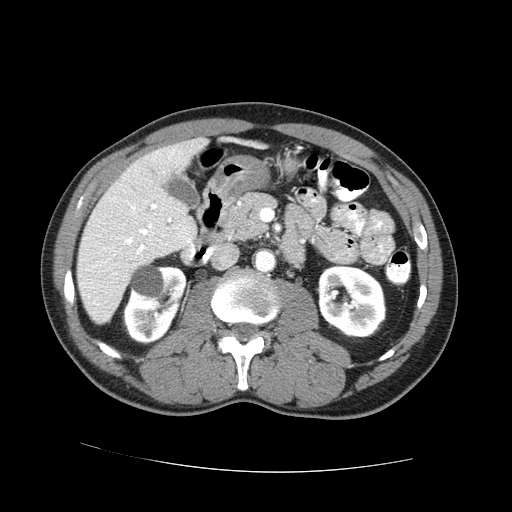
Contrast-enhanced abdominal CT (liver protocol), one axial slice. Slice 26 of 73 in the series (ordered by position). Reconstruction kernel STANDARD. 100 kVp. One of 2 acquisitions stored at this slice position. Soft-tissue window (W 400 / L 40 HU). 2.5 mm slice thickness. 512 × 512 image matrix. From the clinical record (not read from this slice): diagnosis: hepatocellular carcinoma (patient treated with transarterial chemoembolisation; whether this scan precedes or follows treatment is not stated here); TNM stage (as recorded): Stage-IVA; Child-Pugh class: A; tumour differentiation: no biopsy.
Annotated regions visible in this slice (semi-automatic segmentation, software-assisted and operator-edited):
- liver parenchyma outside the tumour (the mass and vessels are separate outlines, so this box may not span the whole liver): bounding box (x1, y1, x2, y2) in pixels: (76, 136, 208, 323)
- liver vessels: (93, 150, 191, 267)